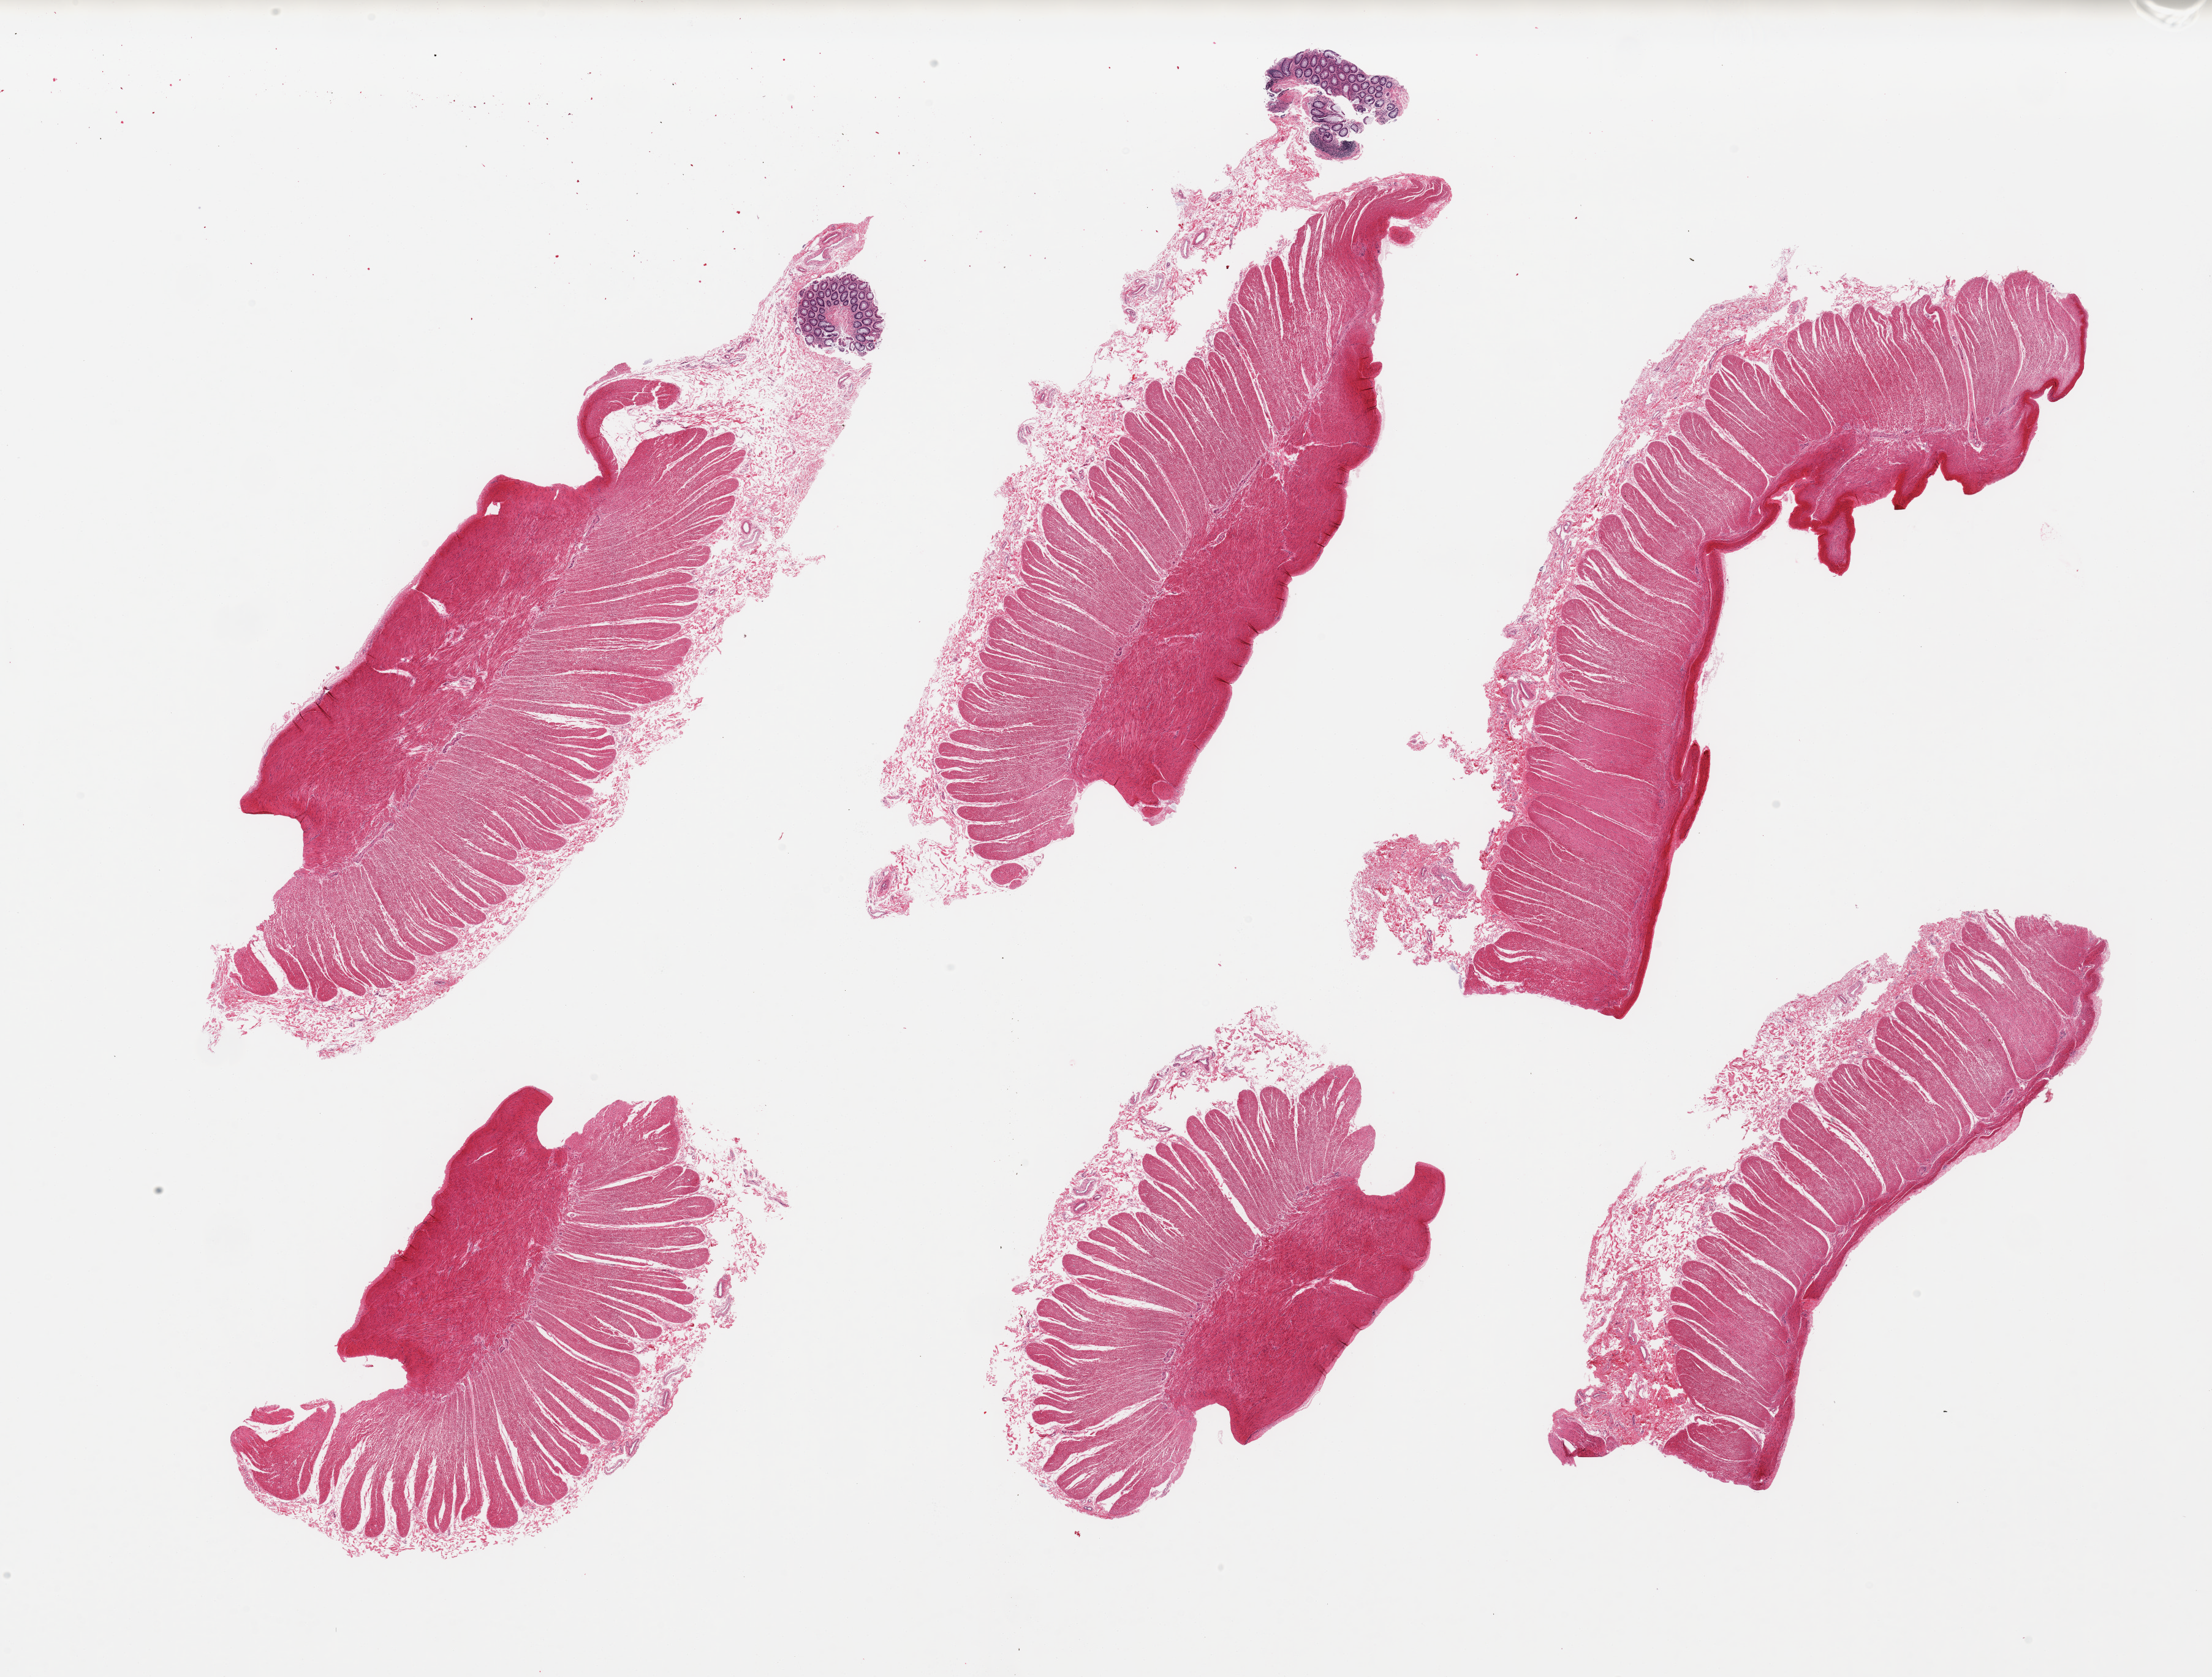
Whole-slide image, haematoxylin and eosin stain, brightfield, low-resolution overview of the scanned area, about 28.5 x 21.6 mm, PAXgene-fixed paraffin-embedded (PFPE) section, section of transverse colon (target tissue), donor tissue sample. Male donor.
Pathologist's review note for this sample: 6 pieces; all with muscularis propria, 2 with minute [1mm] pieces of mucosa.